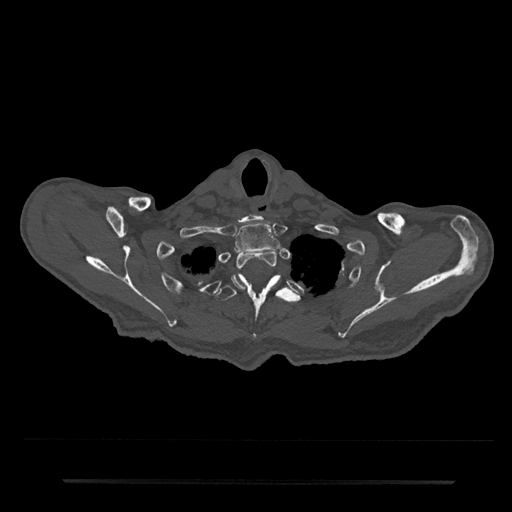
CT including the spine, one axial slice. Slice 686 of 797 in the series (ordered by position). 120 kVp. Bone window (W 1800 / L 400 HU). 512 × 512 image matrix, field of view 427 × 427 mm. Patient: male, 74 years. From the clinical record (not read from this slice): primary cancer: prostate.
Structures marked on this image (semi-automatically segmented with operator editing):
- T1 vertebra: box from (x=234, y=223) to (x=280, y=253) px
- T2 vertebra: (x=231, y=250)–(x=278, y=290)
- T3 vertebra: (x=216, y=274)–(x=300, y=341)